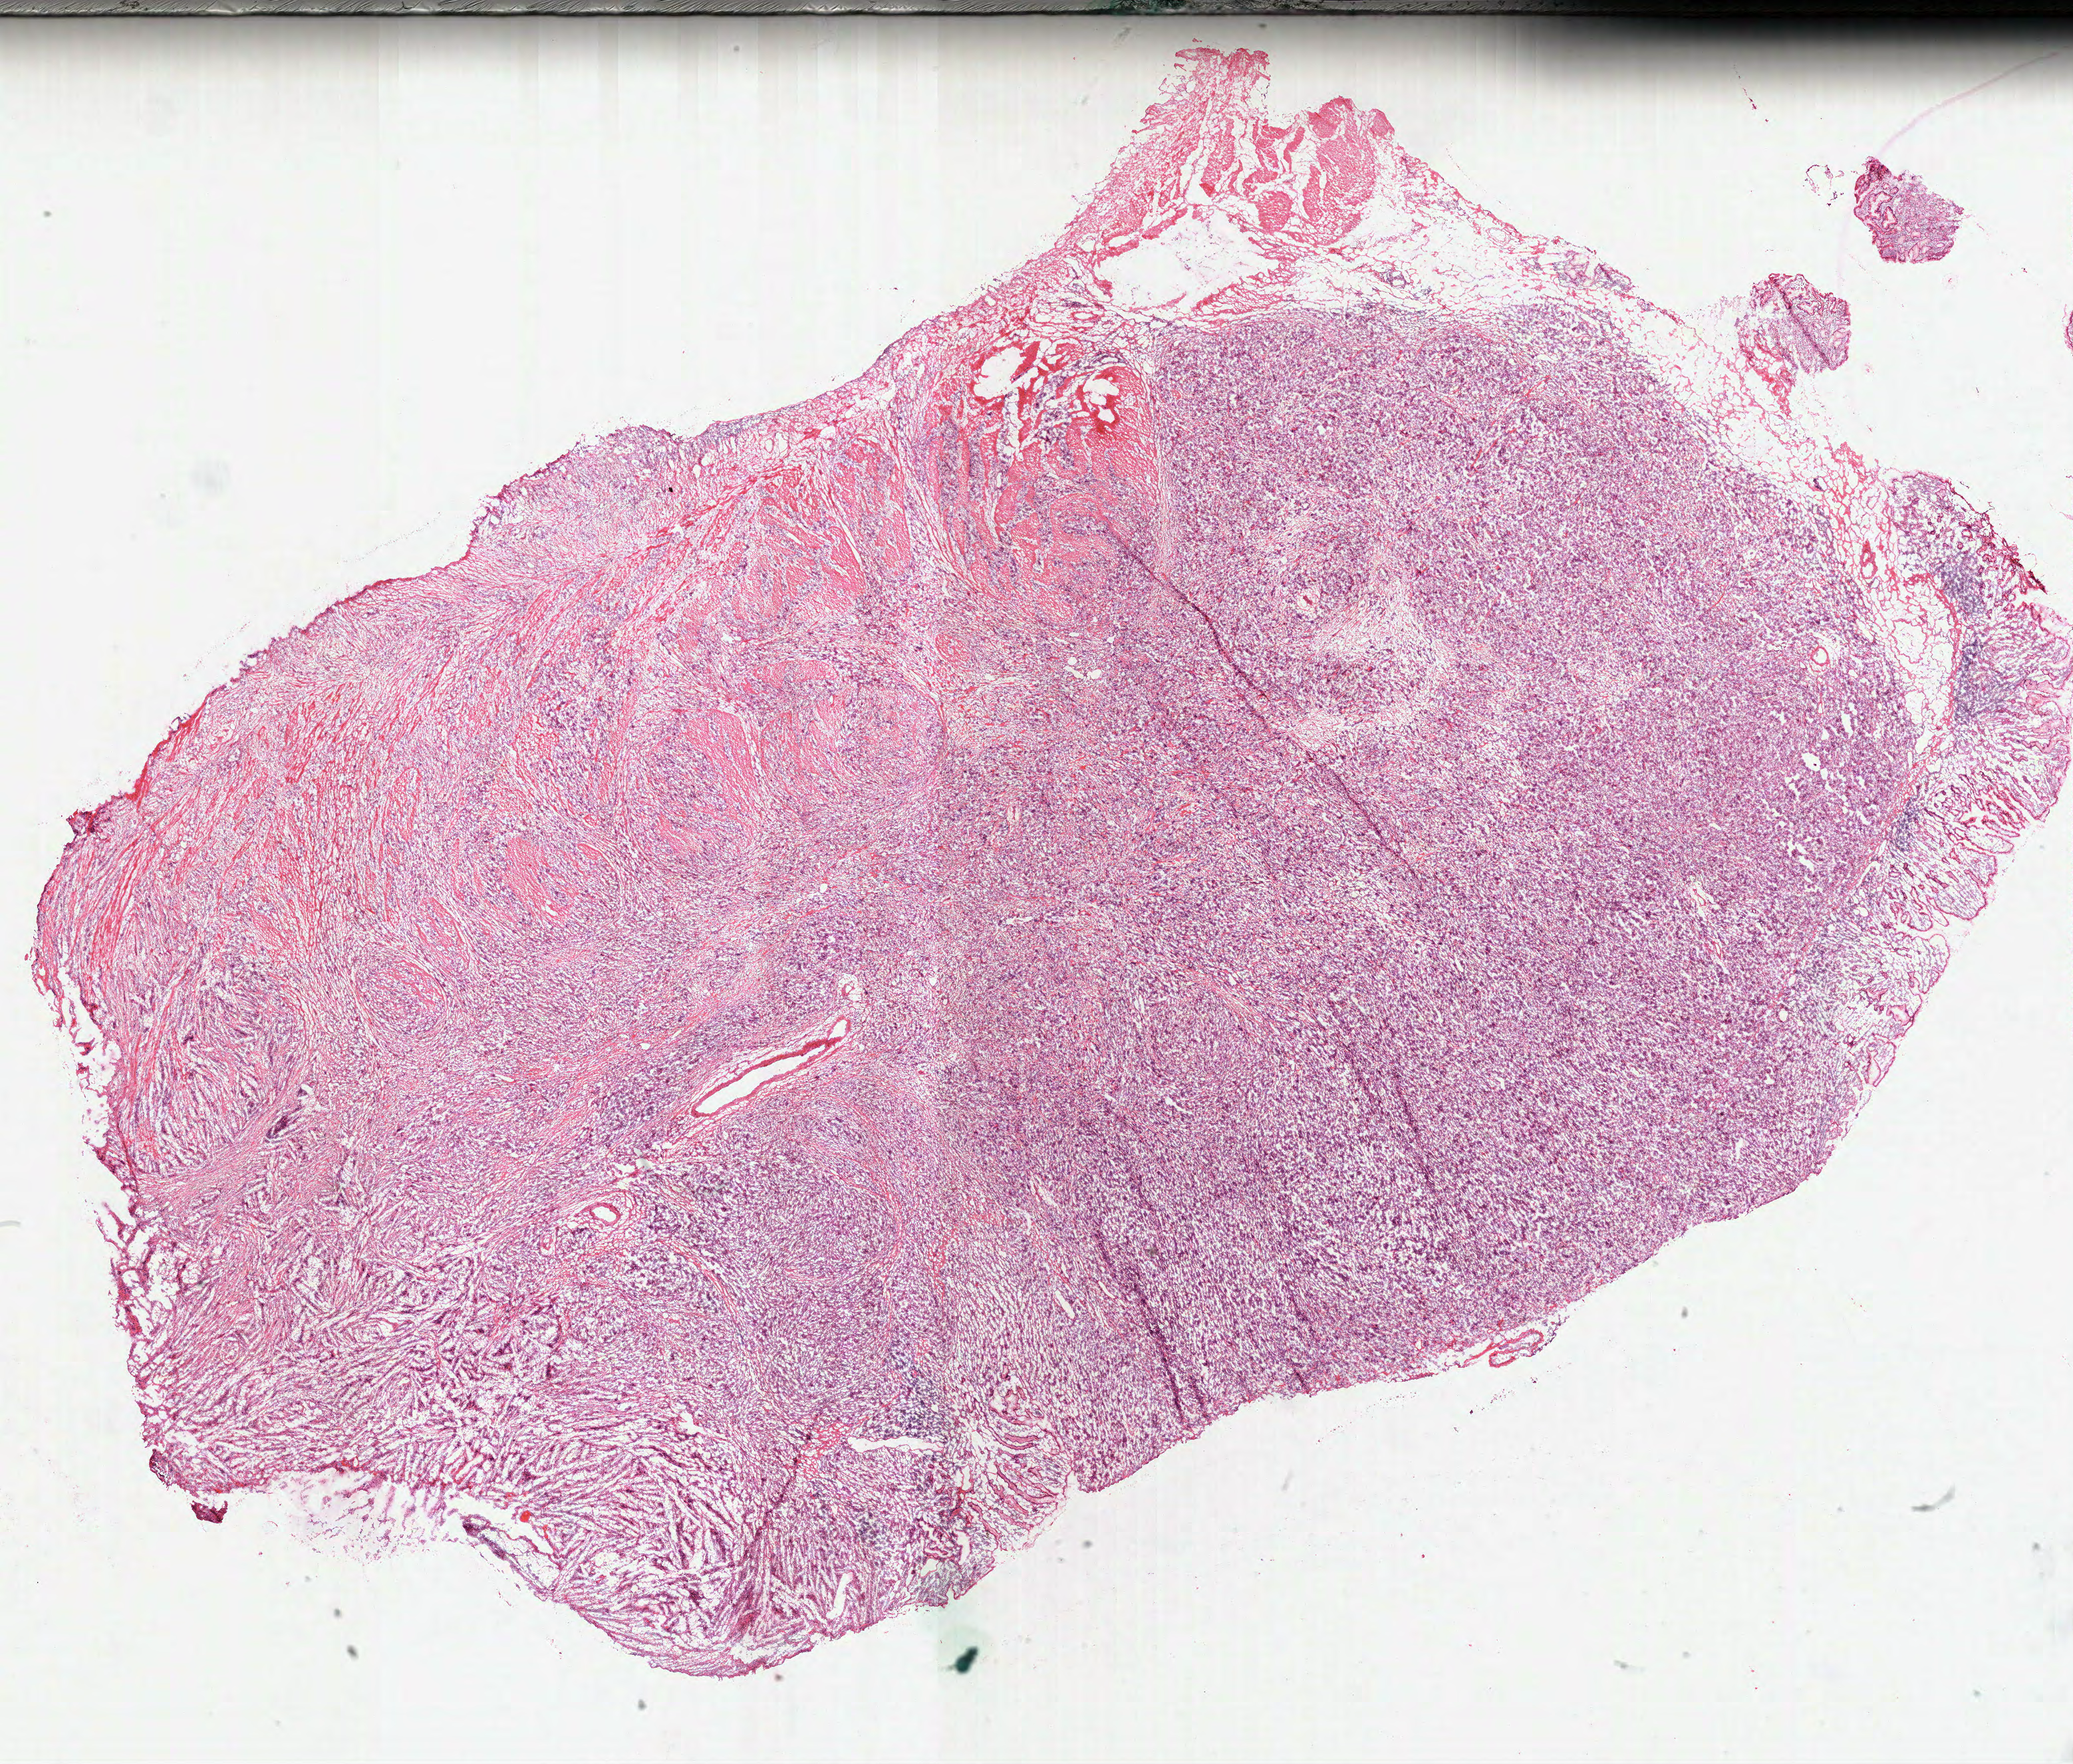
Digitized H&E tissue section (whole slide) — shown as a low-resolution overview of the whole scanned area (about 25.1 x 21.4 mm, acquisition: 40x scan). Frozen section from the top of the tissue portion. Stomach, primary tumour sample. Male, age 51 years at initial diagnosis. Histologic grade: G3 (poorly differentiated). Pathologist review of this section (percent, as recorded): tumour cells 100%, tumour nuclei 75%, normal cells 0%, stromal cells 0%, necrosis 0%. Infiltration values recorded for this section: lymphocyte infiltration 10%, monocyte infiltration 2%, neutrophil infiltration 5%.
Diagnosis: Adenocarcinoma, NOS (fundus of stomach). Lymph nodes positive (case pathology): 1 of 15 examined. AJCC pathologic stage: IIB (7th edition).